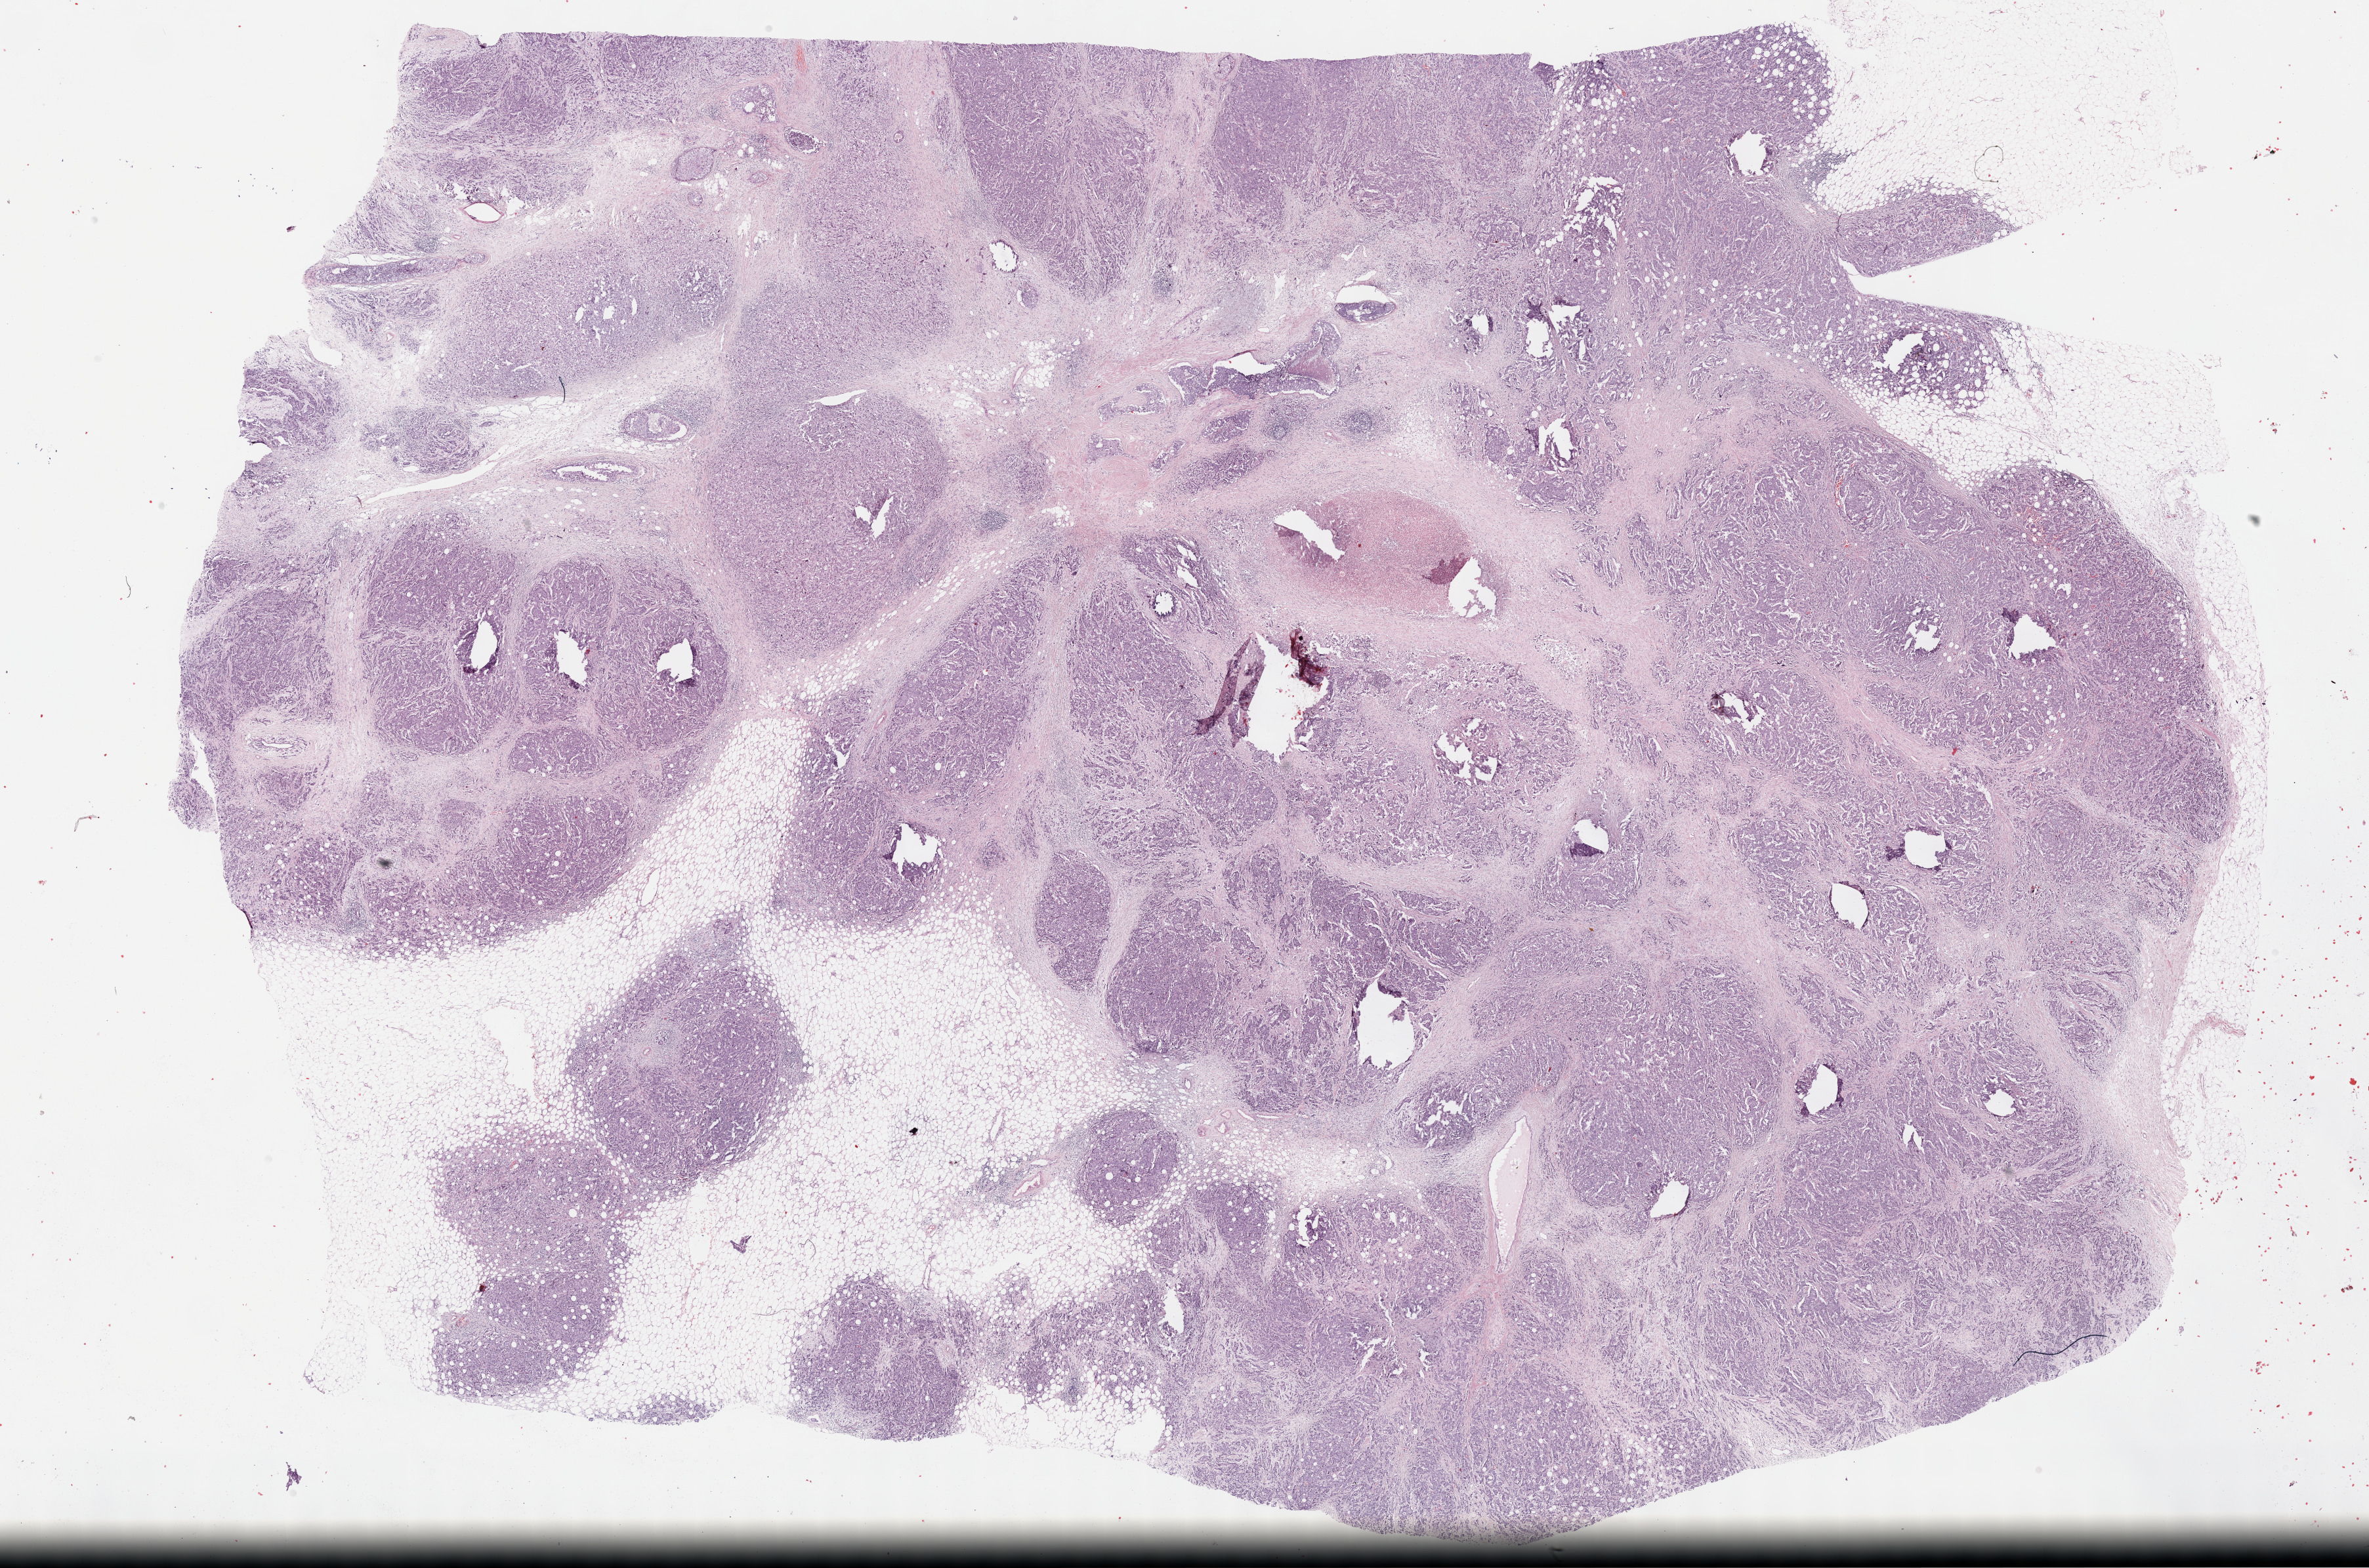
H&E-stained whole-slide image — shown as a low-resolution overview of the whole scanned area (about 29.2 x 19.3 mm); formalin-fixed paraffin-embedded (FFPE) diagnostic section; sample: primary tumour, breast. Female patient; age at initial diagnosis 61 years.
Laterality: right. Lymph nodes positive (case pathology): 5 of 8 examined. Diagnosis: Infiltrating duct carcinoma, NOS. AJCC pathologic stage: IIIA.